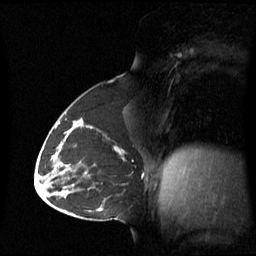
Breast MRI (dynamic contrast-enhanced), one sagittal slice; position 33 of 60 along the scan axis; dynamic contrast-enhanced series, image 2 of 3 at this slice position (ordered by acquisition); 1.5 T; TE 4.2 ms, TR 8.4 ms; 2.8 mm slice thickness; 256 × 256 image matrix, field of view 270 × 270 mm. Female patient, age 43 years. Case-level facts recorded for this patient, not image findings: setting: breast cancer imaged before/during neoadjuvant chemotherapy; receptor status: triple-negative.
Annotated regions visible in this slice (semi-automatically segmented with operator editing):
- analysis volume of interest (the breast-tissue region the enhancement analysis was run in; not a lesion): bounding box <62,124,126,180> (left, top, right, bottom; pixels)
- tumour enhancement mask (voxels above the 70 % enhancement threshold inside the analysis volume of interest): <80,124,124,152>